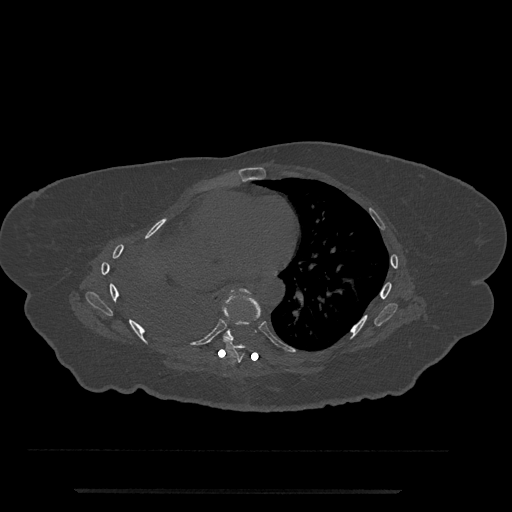
CT including the spine, one axial slice; slice 423 of 797 in the series (ordered by position); reconstruction kernel Br40s/3; 120 kVp; bone window (W 1800 / L 400 HU); 512 × 512 image matrix, field of view 440 × 440 mm. Patient: female, 51 years. From the clinical record (not read from this slice): primary cancer: neuro.
Outlined on this slice (semi-automatic segmentation, software-assisted and operator-edited):
- T7 vertebra: bounding box [x1, y1, x2, y2] px = [223, 297, 262, 363]
- T8 vertebra: [223, 289, 249, 342]